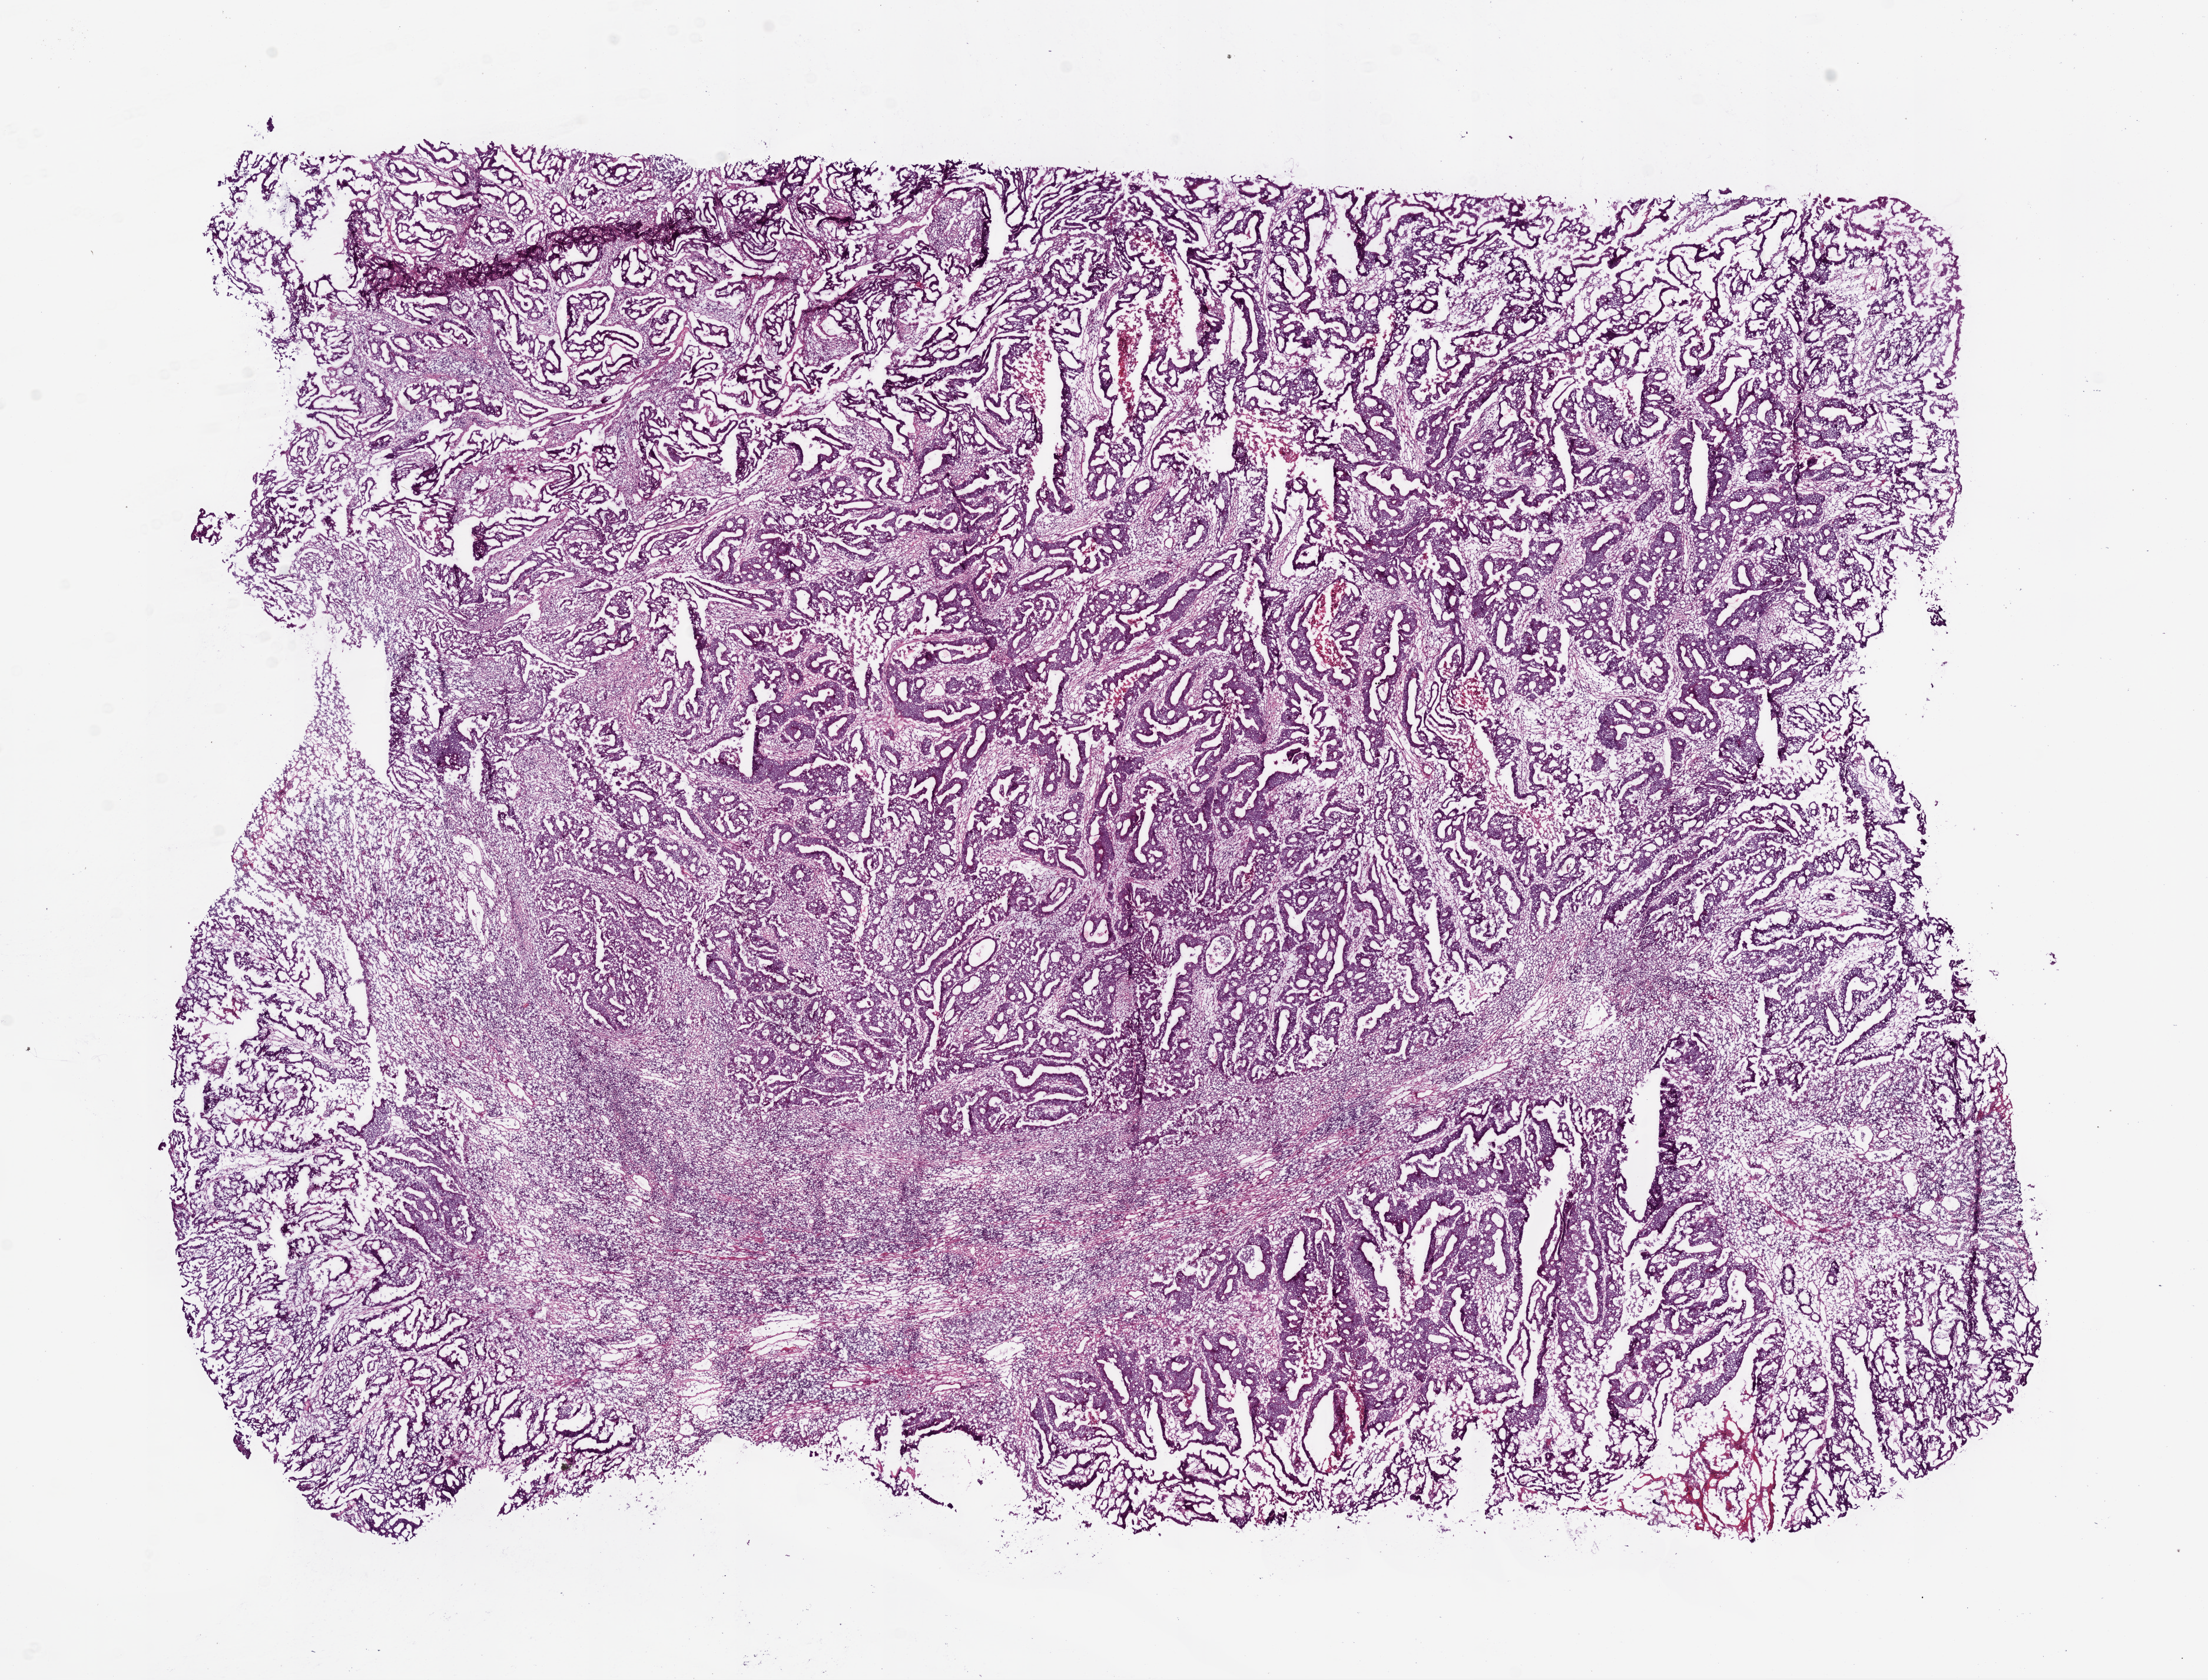
Digitized Hematoxylin and eosin (H&E) stained tissue section (whole slide), shown as a low-resolution overview of the whole scanned area (about 15.0 x 11.4 mm), frozen section from the bottom of the tissue portion, primary tumour sample from the colon. Patient: male, age at initial diagnosis 61 years. Slide review estimates, as recorded: tumour cells 75%, tumour nuclei 70%, normal cells 0%, stromal cells 20%, necrosis 5%.
TNM: T3 N0 M0. AJCC pathologic stage: IIA. Histologic diagnosis: Adenocarcinoma, NOS (cecum).